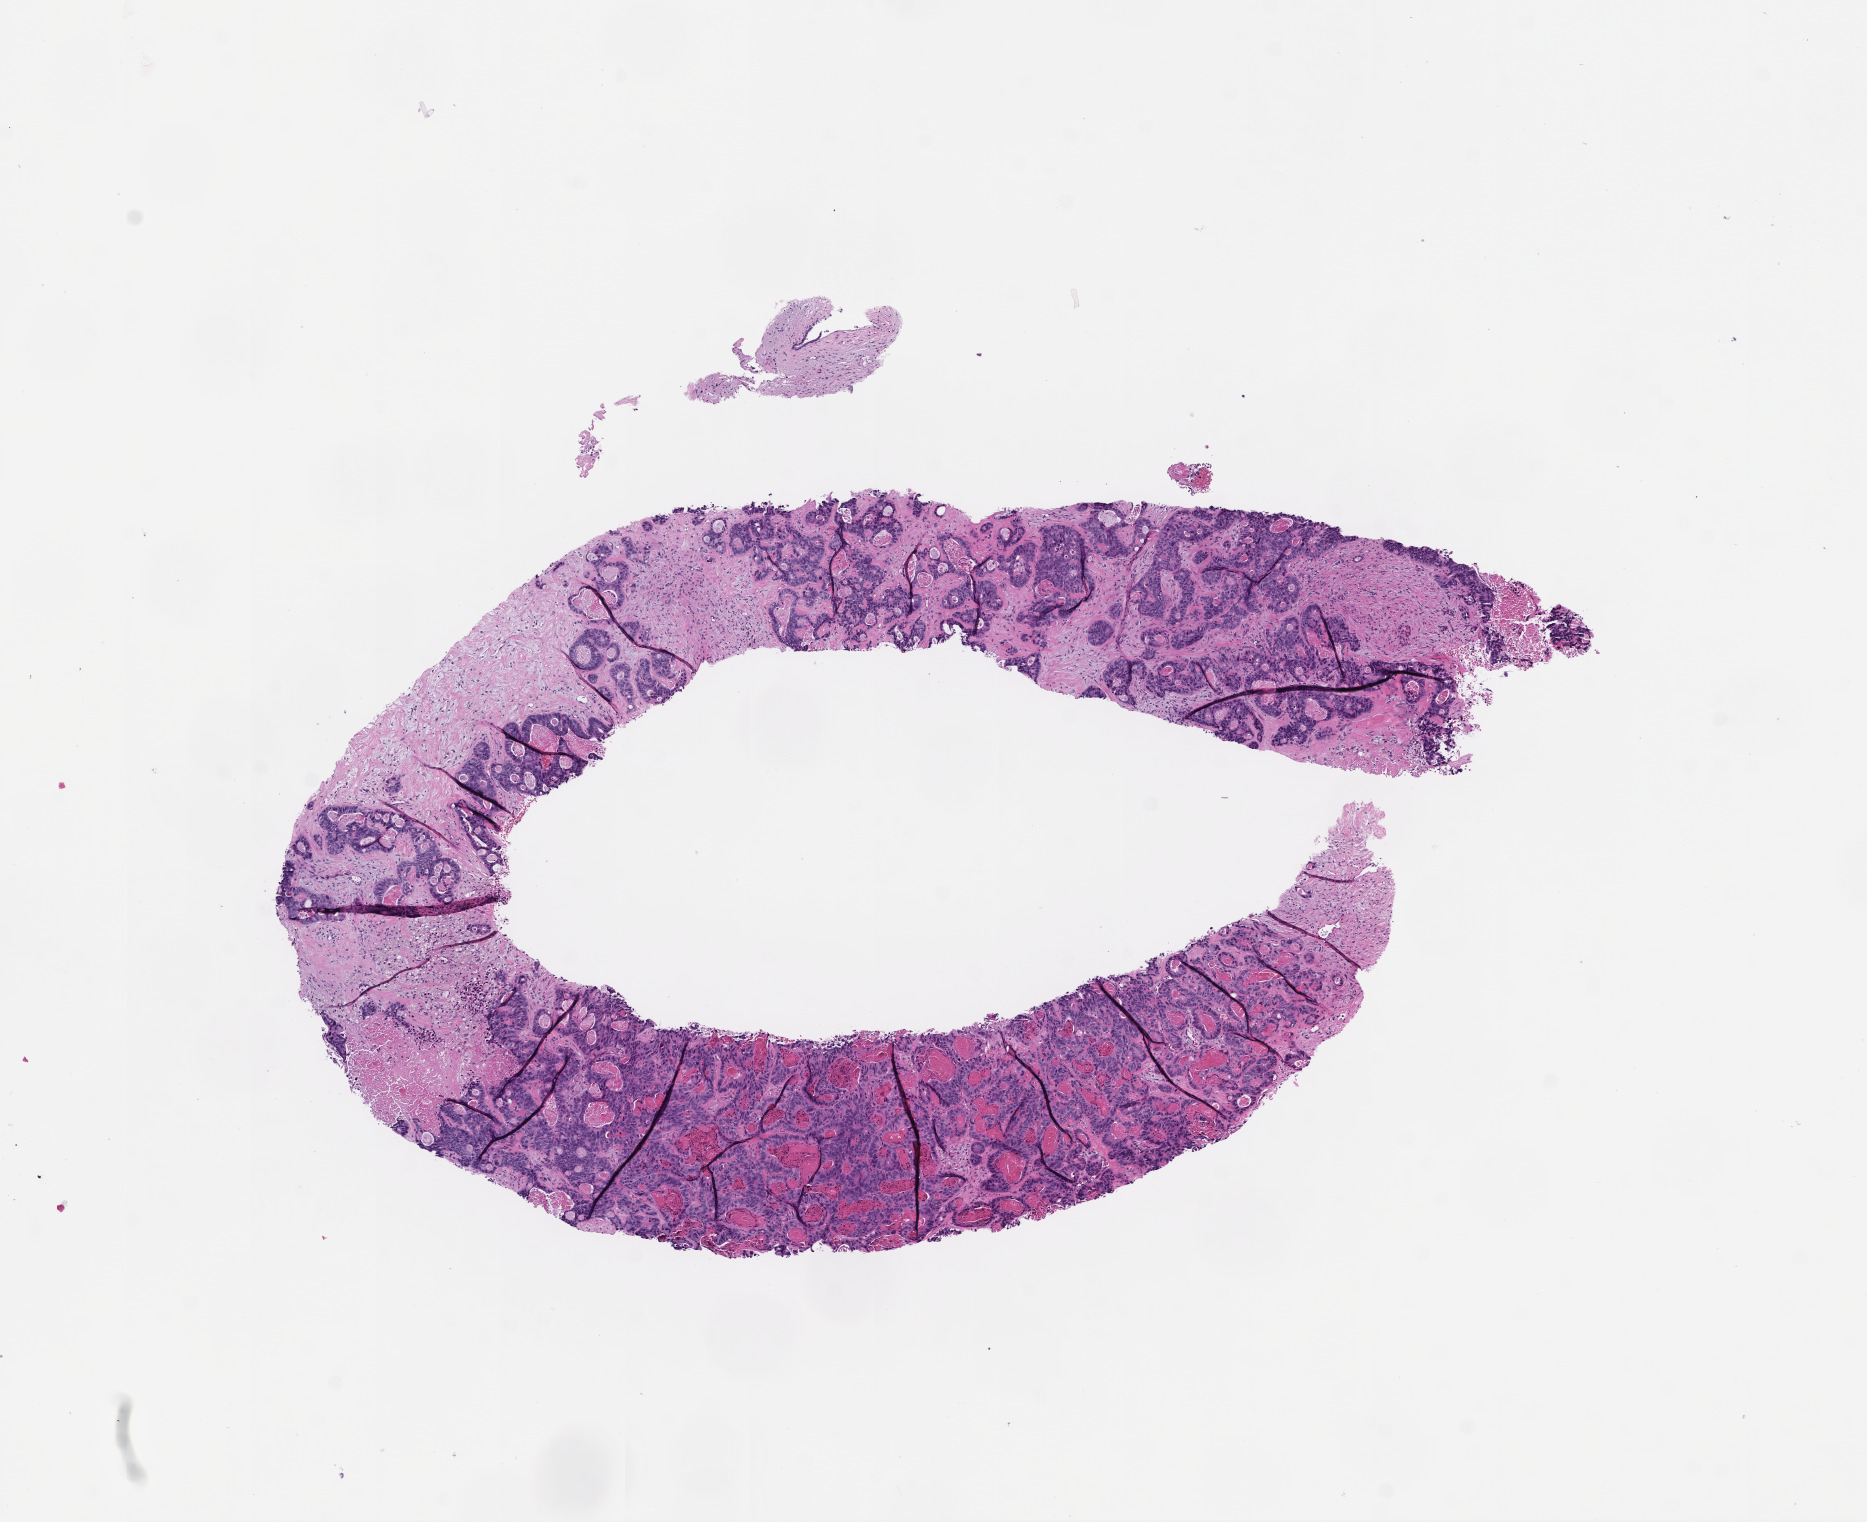
Whole-slide image, haematoxylin and eosin stain, whole scanned area (about 7.5 x 6.1 mm) shown as a low-resolution overview. Formalin-fixed, paraffin-embedded (FFPE) tissue. Collected at disease progression. Patient: male.
This section: metastatic tumor tissue. Patient diagnosis (primary): Colorectal Carcinoma.